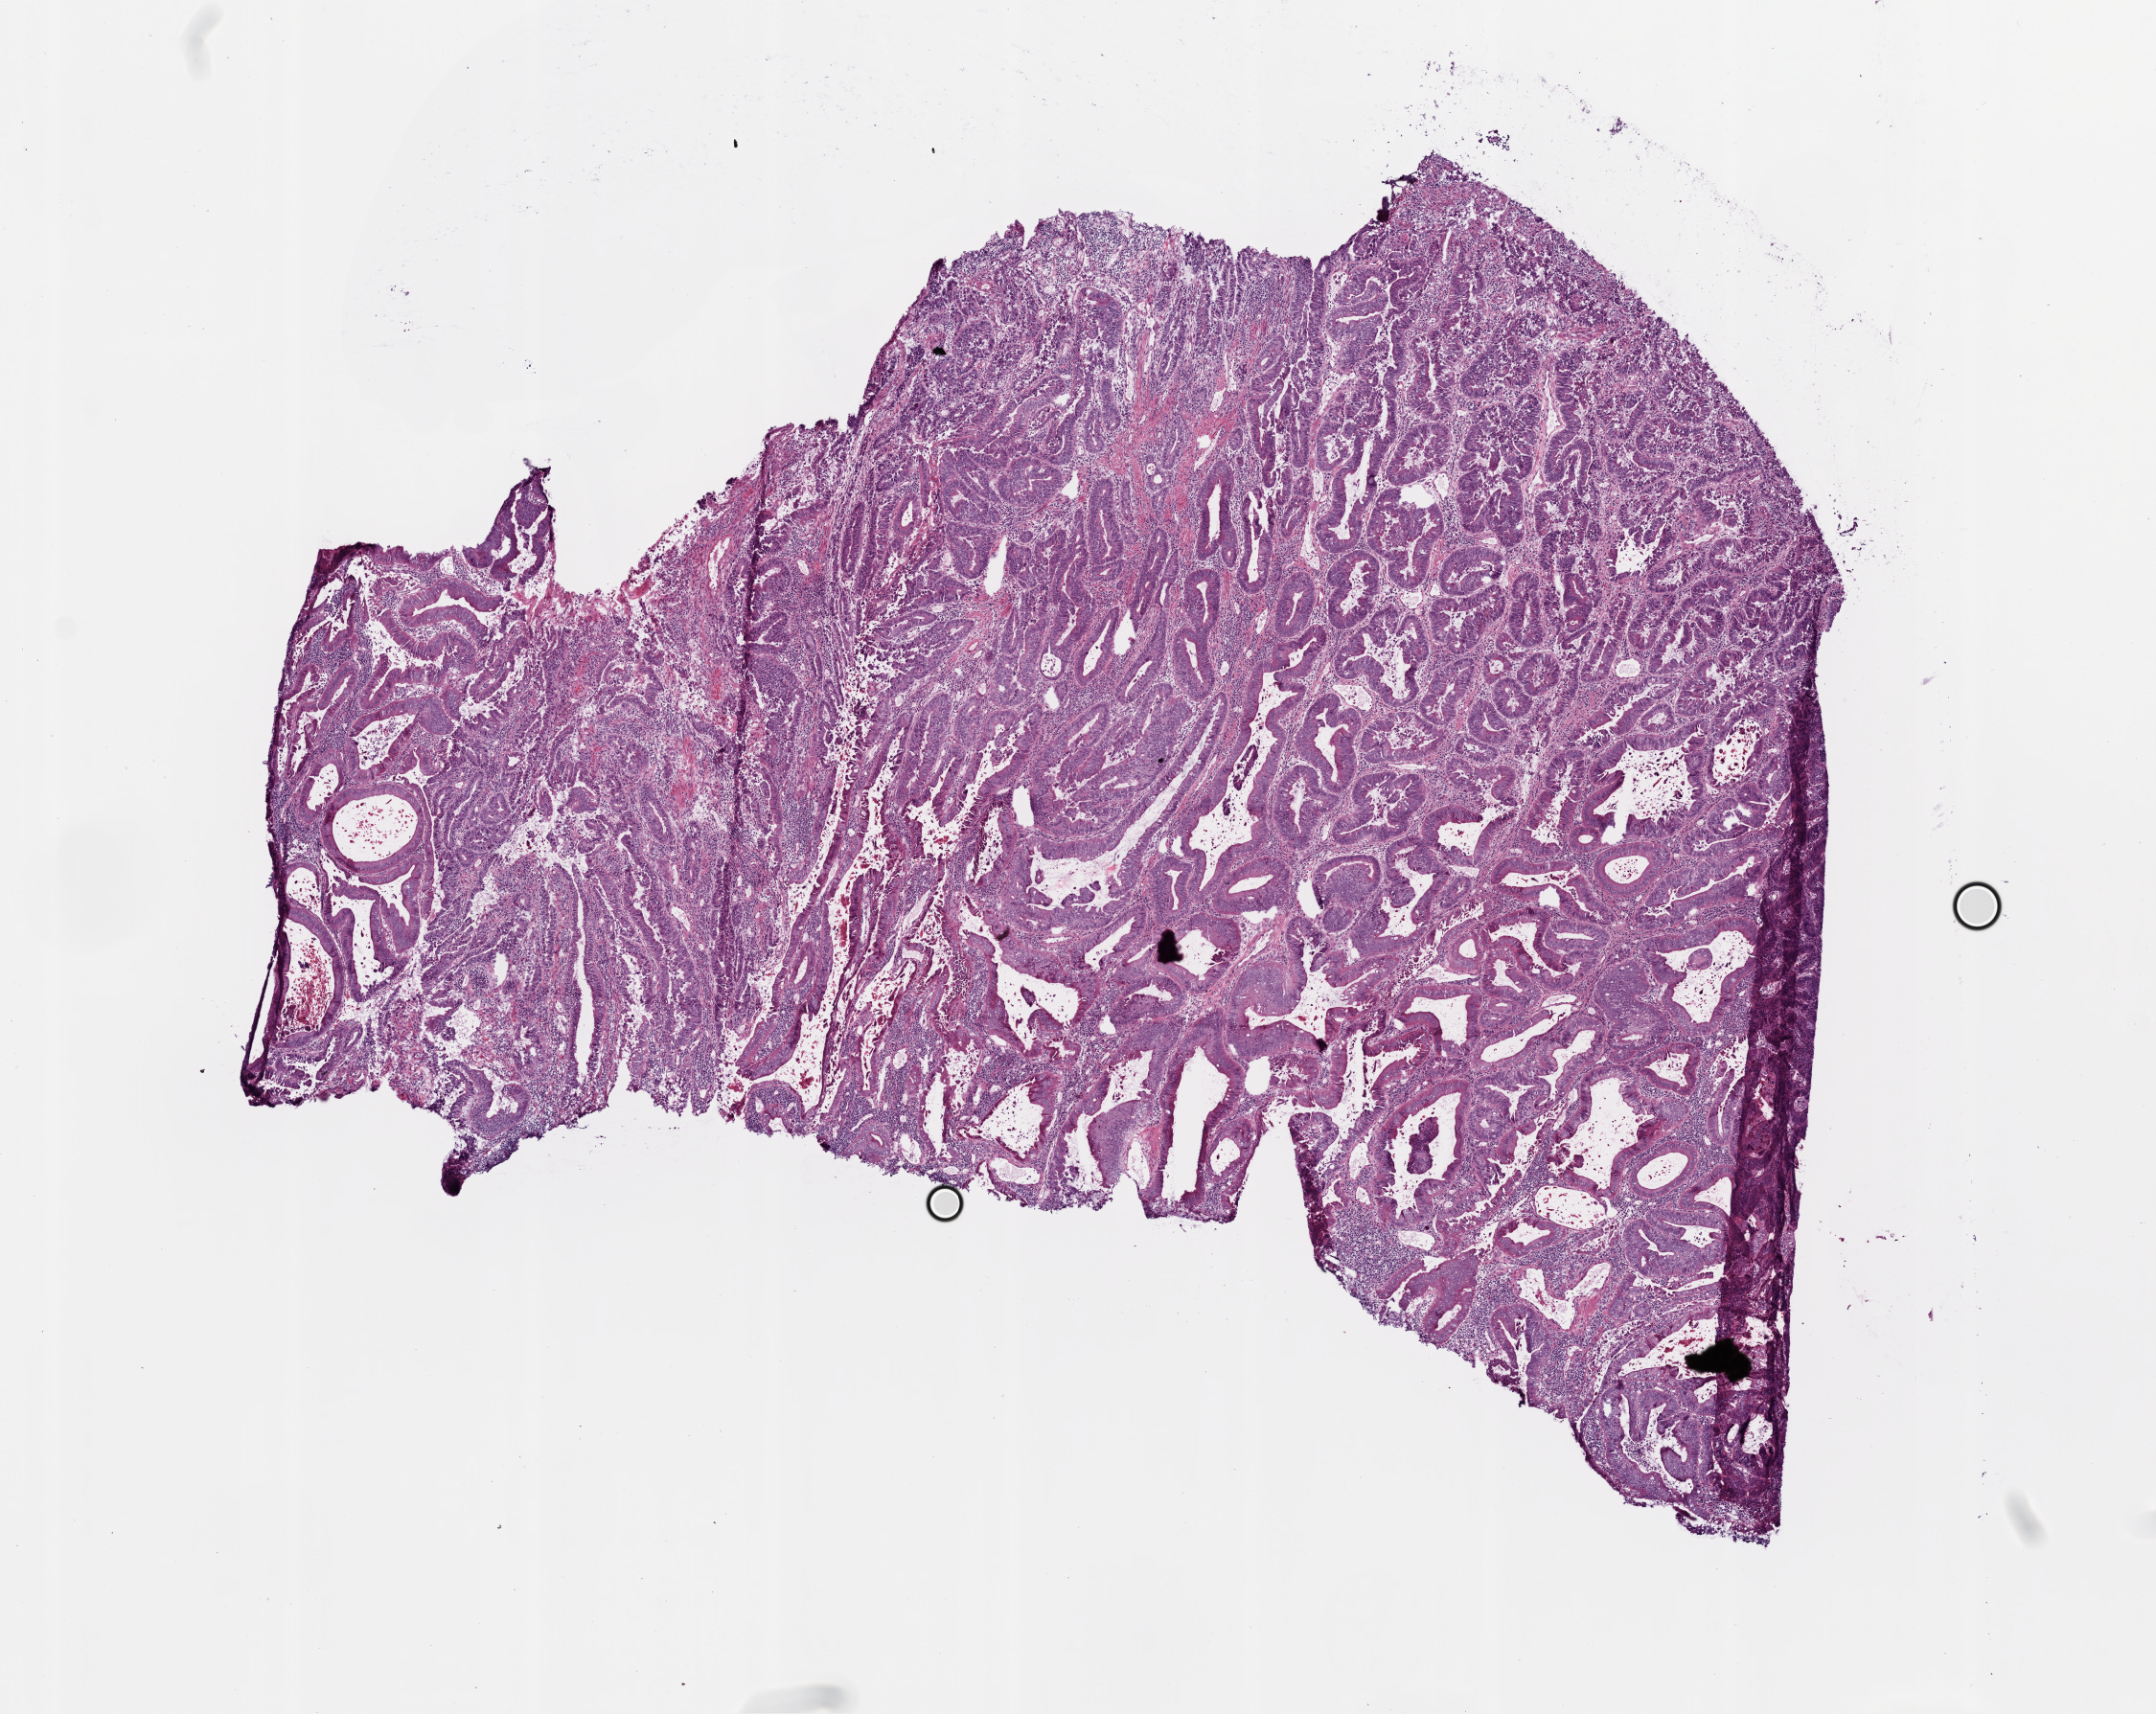
Digitized Hematoxylin and eosin (H&E) stained tissue section (whole slide), low-resolution overview of the scanned area, about 9.0 x 7.2 mm (acquisition: 20x scan); frozen section; colon, primary tumour sample. Patient: female, age at initial diagnosis 63 years. Composition of this section per pathologist review: tumour cells 70%, tumour nuclei 70%, normal cells 10%, stromal cells 10%, necrosis 10%.
Pathologic diagnosis: Adenocarcinoma, NOS (sigmoid colon). TNM: T1 N0. AJCC pathologic stage: I.